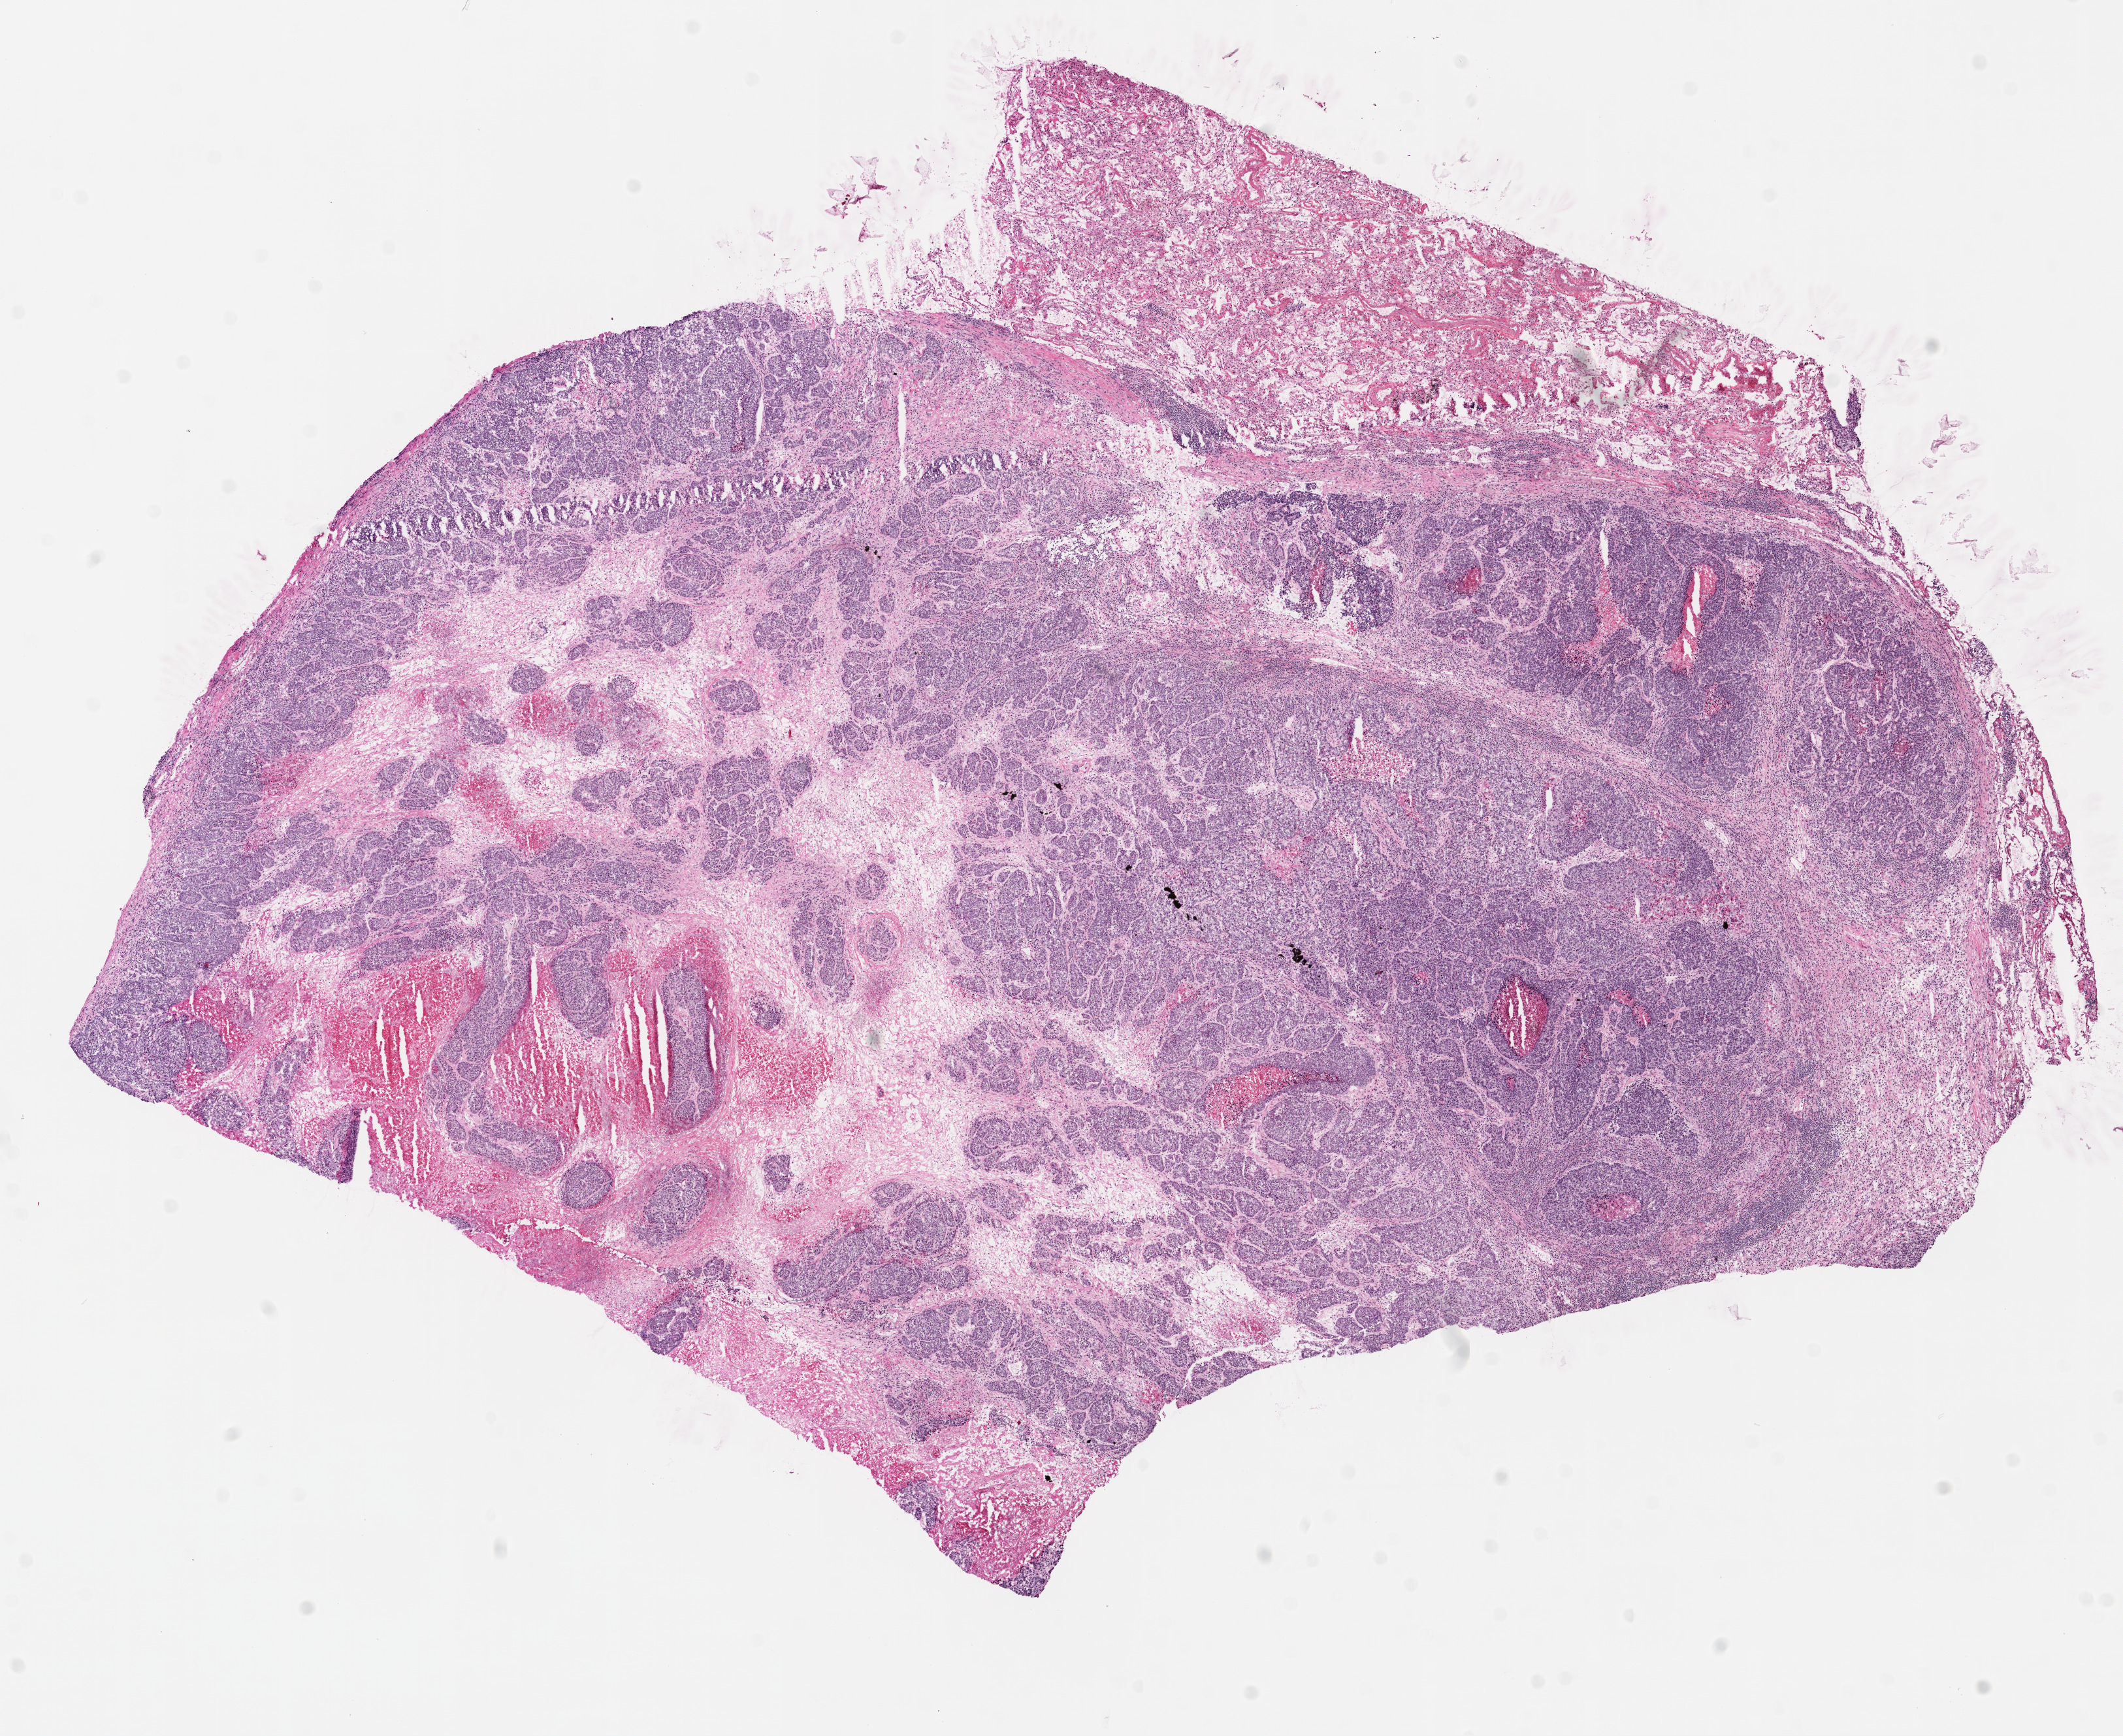
Digitized Hematoxylin and eosin (H&E) stained tissue section (whole slide) — whole scanned area (about 13.0 x 10.7 mm) shown as a low-resolution overview. Frozen section. Lung, primary tumour sample. Patient: female, age at initial diagnosis 61 years. Slide review estimates, as recorded: tumour cells 55%, tumour nuclei 75%, normal cells 15%, stromal cells 20%, necrosis 10%.
• AJCC pathologic stage: IV (7th edition)
• laterality: left
• diagnosis: Squamous cell carcinoma, NOS (lower lobe, lung)